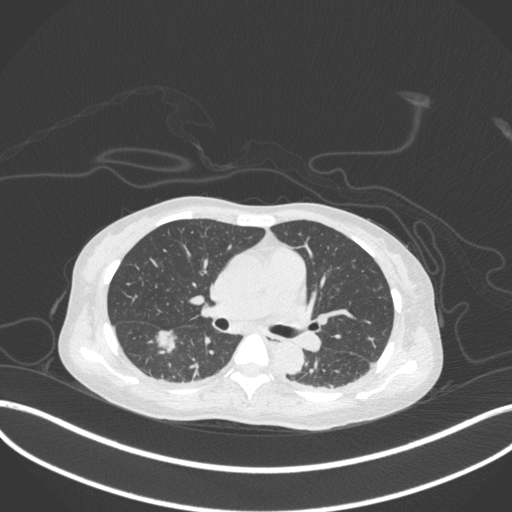
Chest CT, one axial slice. Slice 178 of 260 in the series (ordered by position). Reconstruction kernel B31f. Lung window (W 1500 / L -600 HU). 1 mm slice thickness. 512 × 512 image matrix, field of view 400 × 400 mm. Patient: female, 44 years. Case-level facts recorded for this patient, not image findings: clinical TNM (as recorded): T1c N0 M0.
Structures marked on this image (rectangle marked by the reading radiologist):
- lung tumour (recorded histology: adenocarcinoma): box from (x=151, y=326) to (x=178, y=357) px